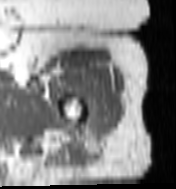
MRI of an extremity soft-tissue mass, one axial slice. Slice 94 of 100 in the series (ordered by position). MR volume resampled by the dataset authors to the PET/CT grid (not the native acquisition matrix). 3.27 mm slice thickness. 176 × 189 image matrix. Female patient. From the clinical record (not read from this slice): histological type: undifferentiated – high grade; grade: high; site of the primary tumour: left thigh.
Outlined on this slice (expert contour drawn on MRI and transferred to this co-registered scan by the dataset authors):
- gross tumour volume including surrounding oedema: bounding box (x1, y1, x2, y2) in pixels: (91, 109, 104, 122)